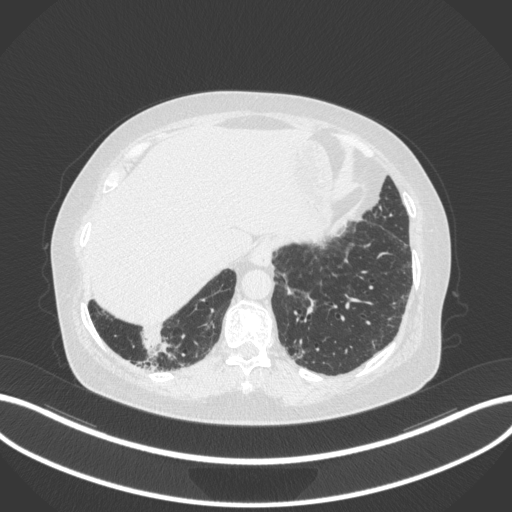
Chest CT, one axial slice. Position 19 of 303 along the scan axis. Reconstruction kernel B31f. 120 kVp. Lung window (W 1500 / L -600 HU). 1 mm slice thickness. 512 × 512 image matrix, field of view 400 × 400 mm. Female patient, age 65 years. From the clinical record (not read from this slice): clinical TNM (as recorded): T2b N1 M0; histopathological grade: G1.
Structures marked on this image (rectangle marked by the reading radiologist):
- lung tumour (recorded histology: adenocarcinoma): bounding box <137,328,173,359> (left, top, right, bottom; pixels)